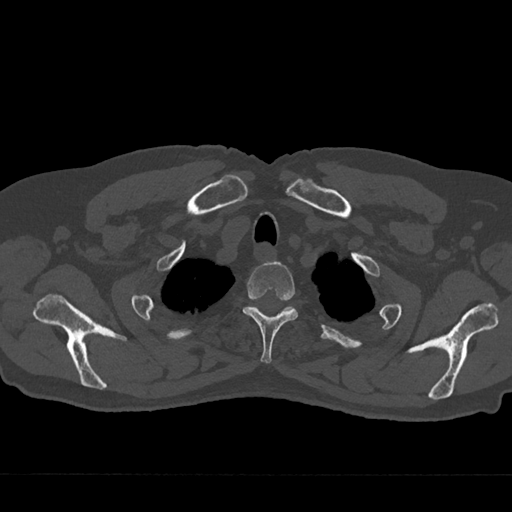
CT including the spine, one axial slice. Slice 607 of 797 in the series (ordered by position). Reconstruction kernel Br40s/3. 120 kVp. Bone window (W 1800 / L 400 HU). 0.5 mm slice thickness. 512 × 512 image matrix, field of view 377 × 377 mm. Male patient, age 75 years. From the clinical record (not read from this slice): primary cancer: renal; vertebrae with lytic lesions (as recorded): T4.
Structures marked on this image (semi-automatically segmented with operator editing):
- T2 vertebra: bounding box [x1, y1, x2, y2] px = [243, 261, 298, 364]
- T3 vertebra: [254, 307, 293, 312]